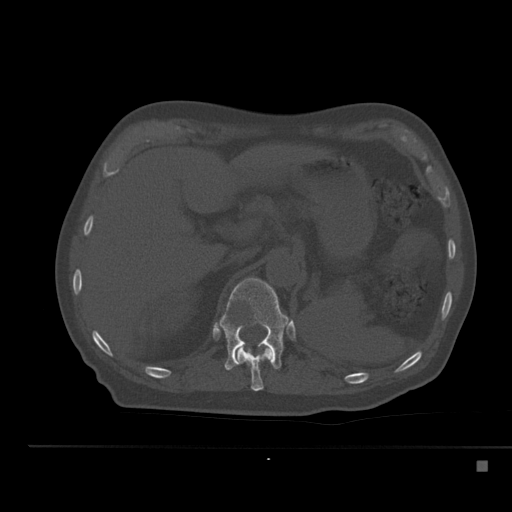
CT including the spine, one axial slice; position 235 of 517 along the scan axis; bone window (W 1800 / L 400 HU); 512 × 512 image matrix, field of view 408 × 408 mm. Patient: male, 70 years. Case-level facts recorded for this patient, not image findings: primary cancer: renal.
Annotated regions visible in this slice (semi-automatically segmented with operator editing):
- T11 vertebra: box from (x=235, y=344) to (x=274, y=391) px
- T12 vertebra: (x=217, y=278)–(x=290, y=370)